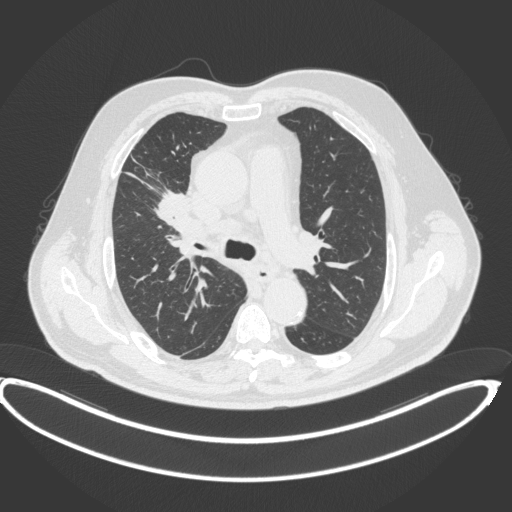
Chest CT, one axial slice. Slice 268 of 395 in the series (ordered by position). 120 kVp. Lung window (W 1500 / L -600 HU). 1 mm slice thickness. 512 × 512 image matrix, field of view 448 × 448 mm. Male patient, age 62 years. From the clinical record (not read from this slice): clinical TNM (as recorded): T1c N3 M1c.
Structures marked on this image (bounding box drawn by a radiologist):
- lung tumour (recorded histology: adenocarcinoma): box from (x=154, y=185) to (x=191, y=228) px